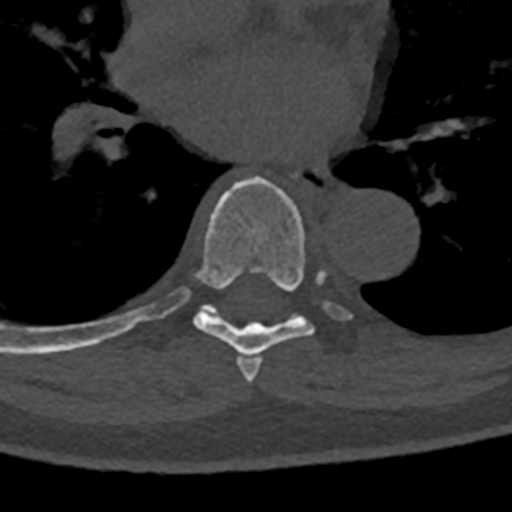
CT including the spine, one axial slice. Slice 757 of 797 in the series (ordered by position). Reconstruction kernel Br40s/3. 120 kVp. Bone window (W 1800 / L 400 HU). 0.5 mm slice thickness. 512 × 512 image matrix, field of view 160 × 160 mm. Patient: male, 74 years. From the clinical record (not read from this slice): primary cancer: renal; vertebrae with lytic lesions (as recorded): T10, L1, L2, L3, L4, L5.
Outlined on this slice (semi-automatic segmentation, software-assisted and operator-edited):
- T6 vertebra: box from (x=243, y=357) to (x=263, y=383) px
- T7 vertebra: (x=70, y=176)–(x=352, y=372)
- T8 vertebra: (x=70, y=318)–(x=142, y=350)